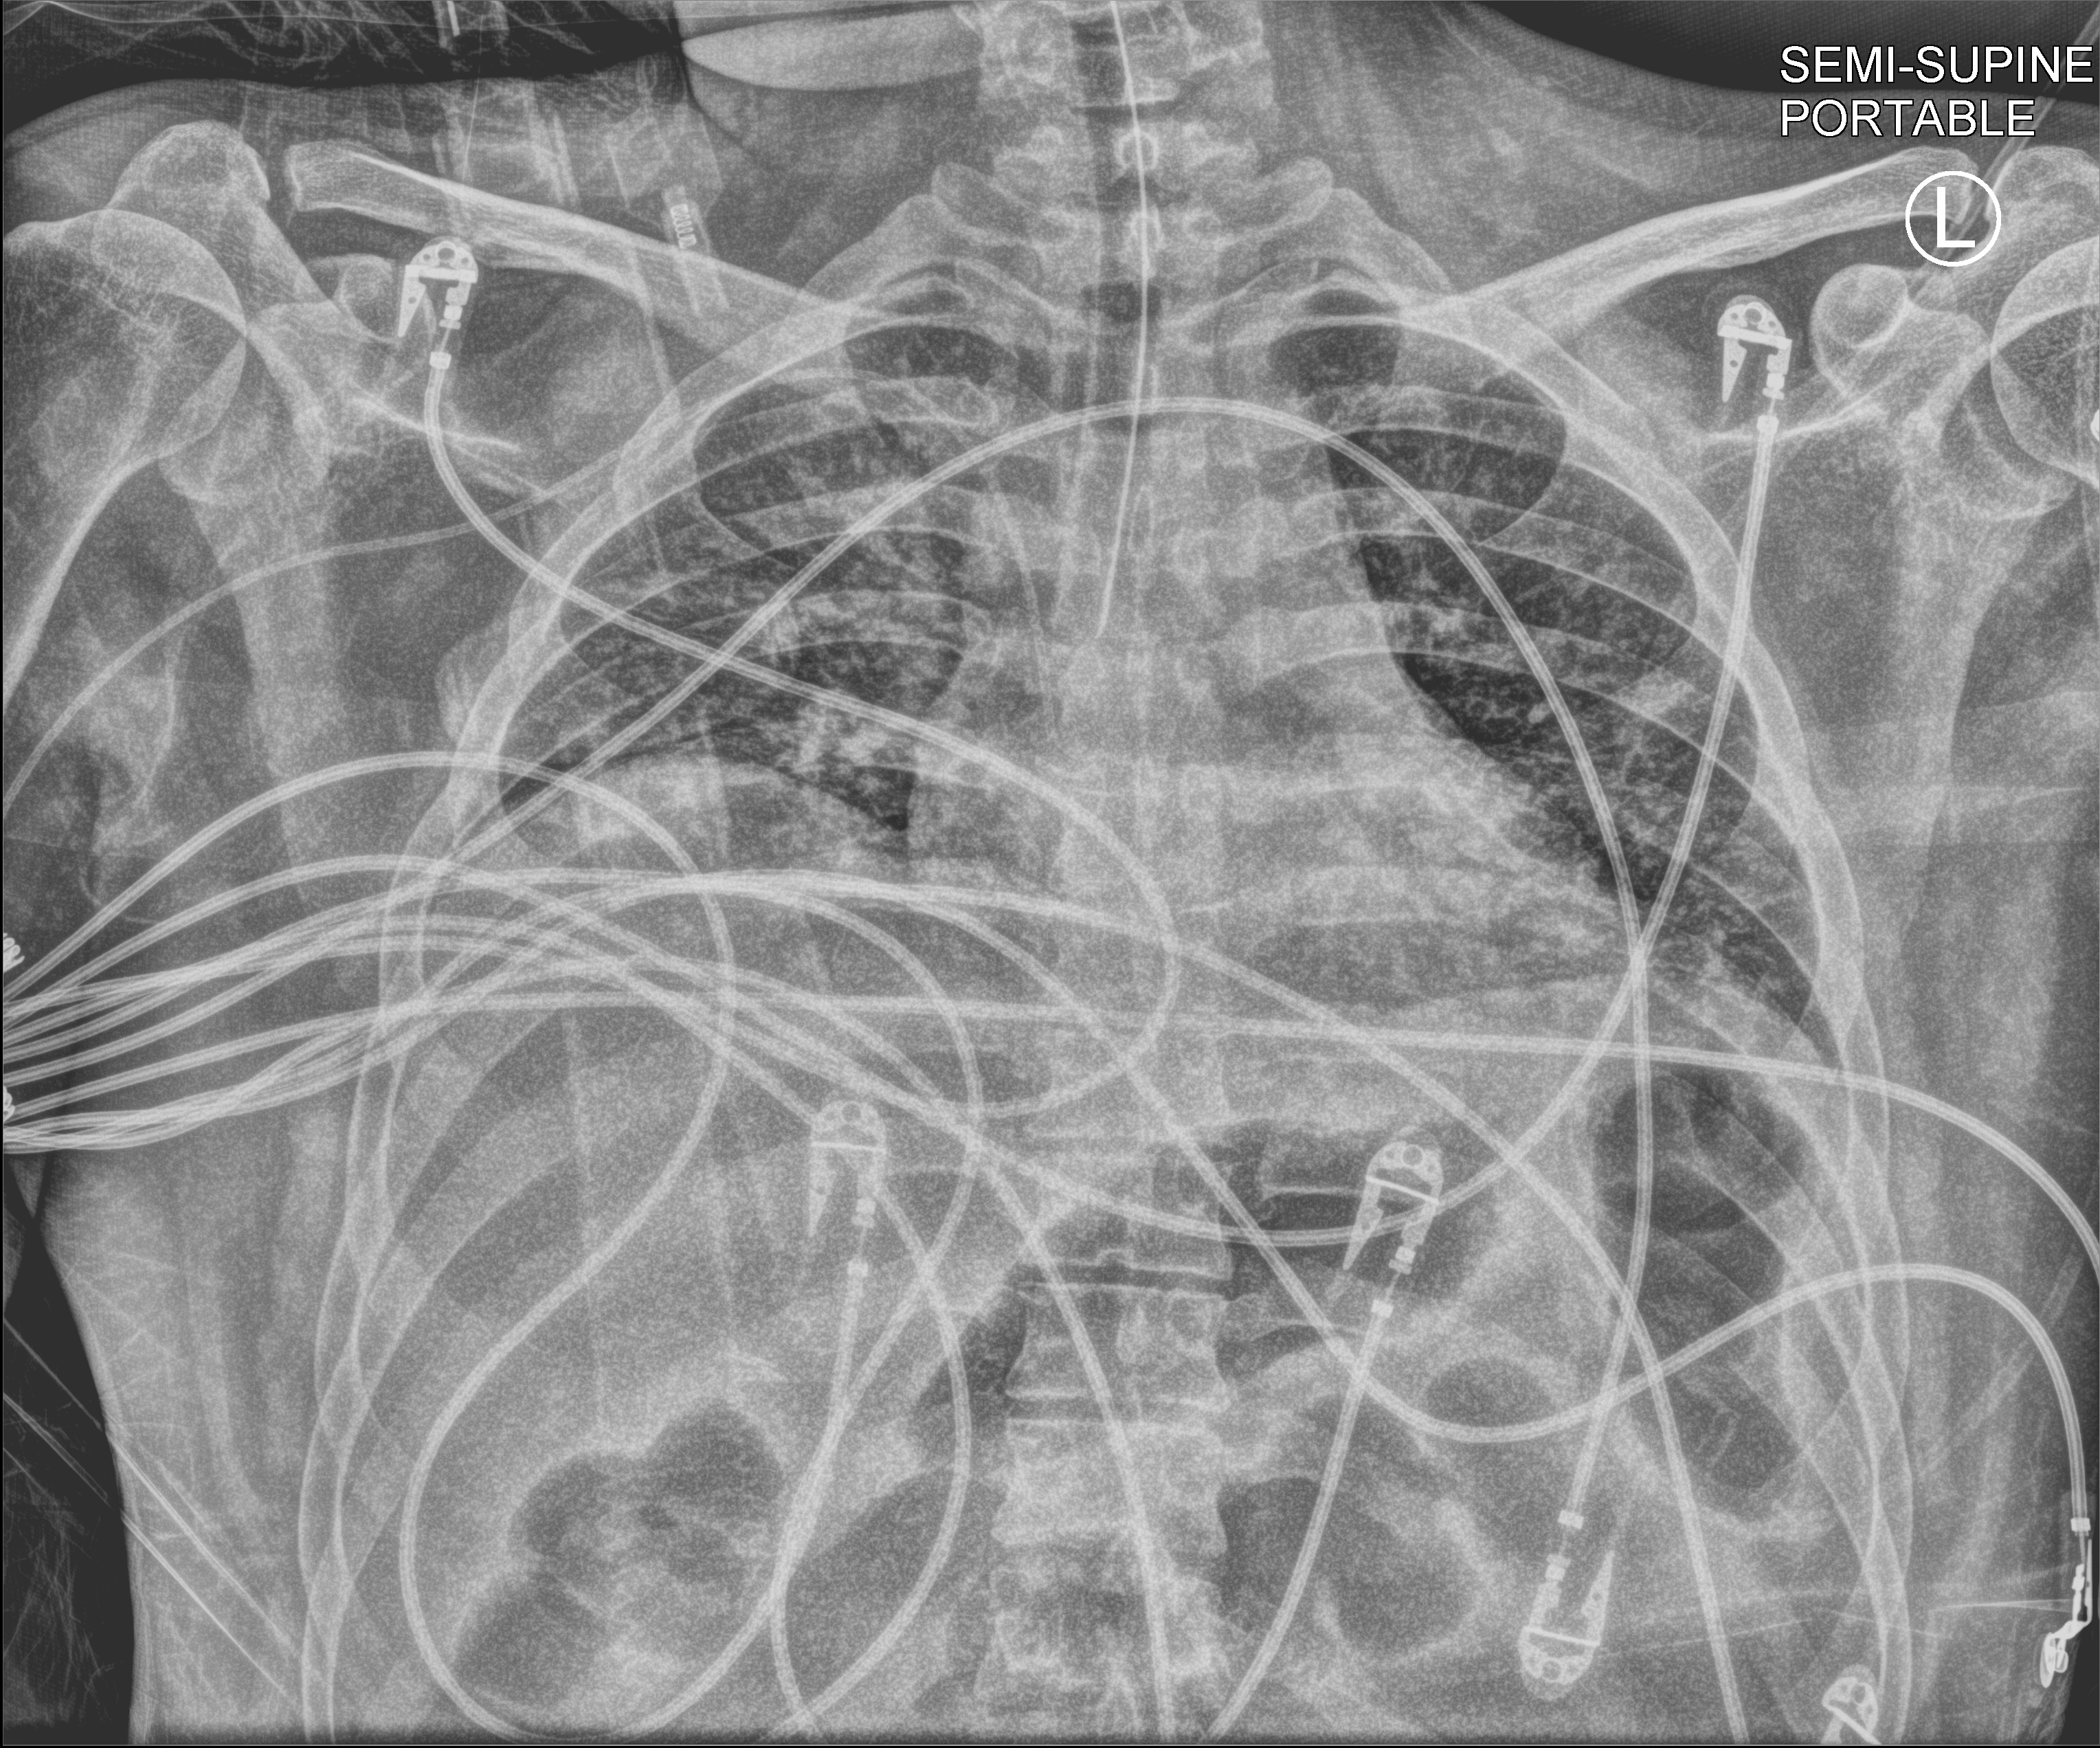
Chest X-ray (portable); anteroposterior (AP) projection. Male patient hospitalised with COVID-19, age 18–59 years.
Admission-level facts for this patient (not findings on this image; timing relative to this image not recorded):
- admitted to intensive care during this hospital stay: yes